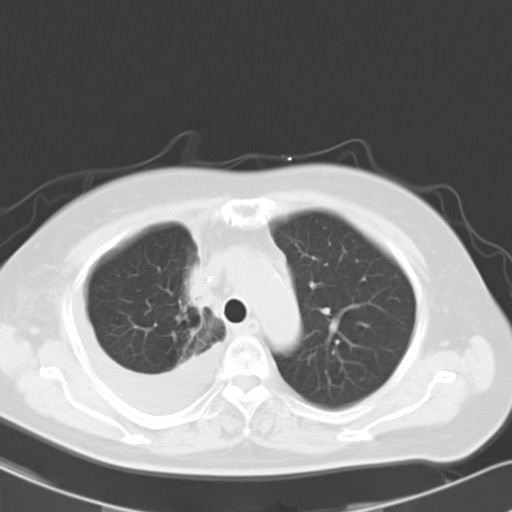
Chest CT, one axial slice. Position 20 of 26 along the scan axis. Reconstruction kernel B40f. Lung window (W 1500 / L -600 HU). 10 mm slice thickness. 512 × 512 image matrix. Female patient, age 69 years. From the clinical record (not read from this slice): clinical TNM (as recorded): T2a N0 M1c.
Outlined on this slice (rectangle marked by the reading radiologist):
- lung tumour (recorded histology: adenocarcinoma): bounding box [x1, y1, x2, y2] px = [189, 260, 221, 333]